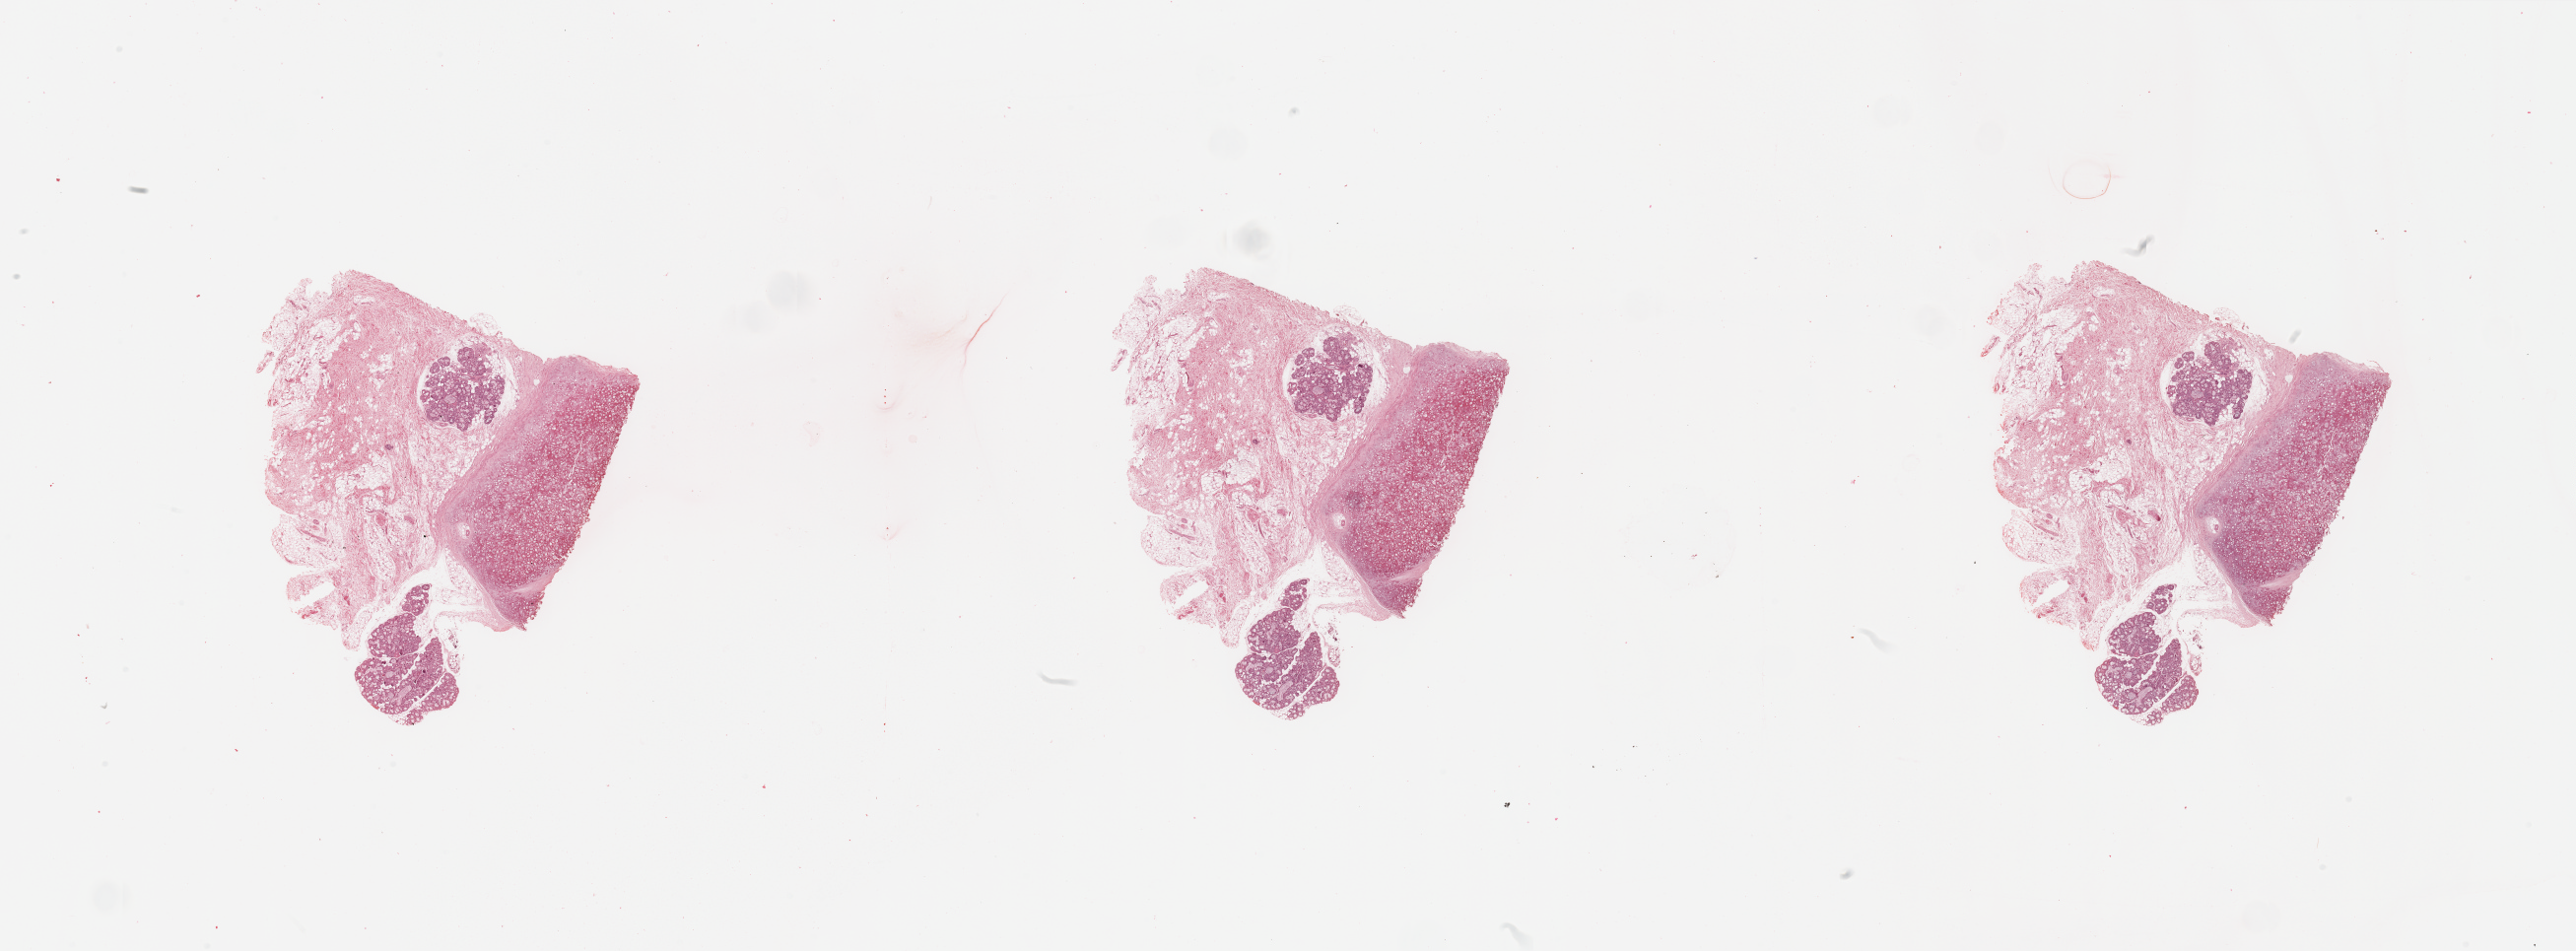
Whole-slide histology image, Hematoxylin and eosin (H&E) stained — low-resolution overview of the scanned area, about 41.3 x 15.3 mm (acquisition: 20x scan), head and neck, tissue type not recorded. Male, 60 y/o.
Patient diagnosis: Squamous cell carcinoma, NOS (larynx, NOS).